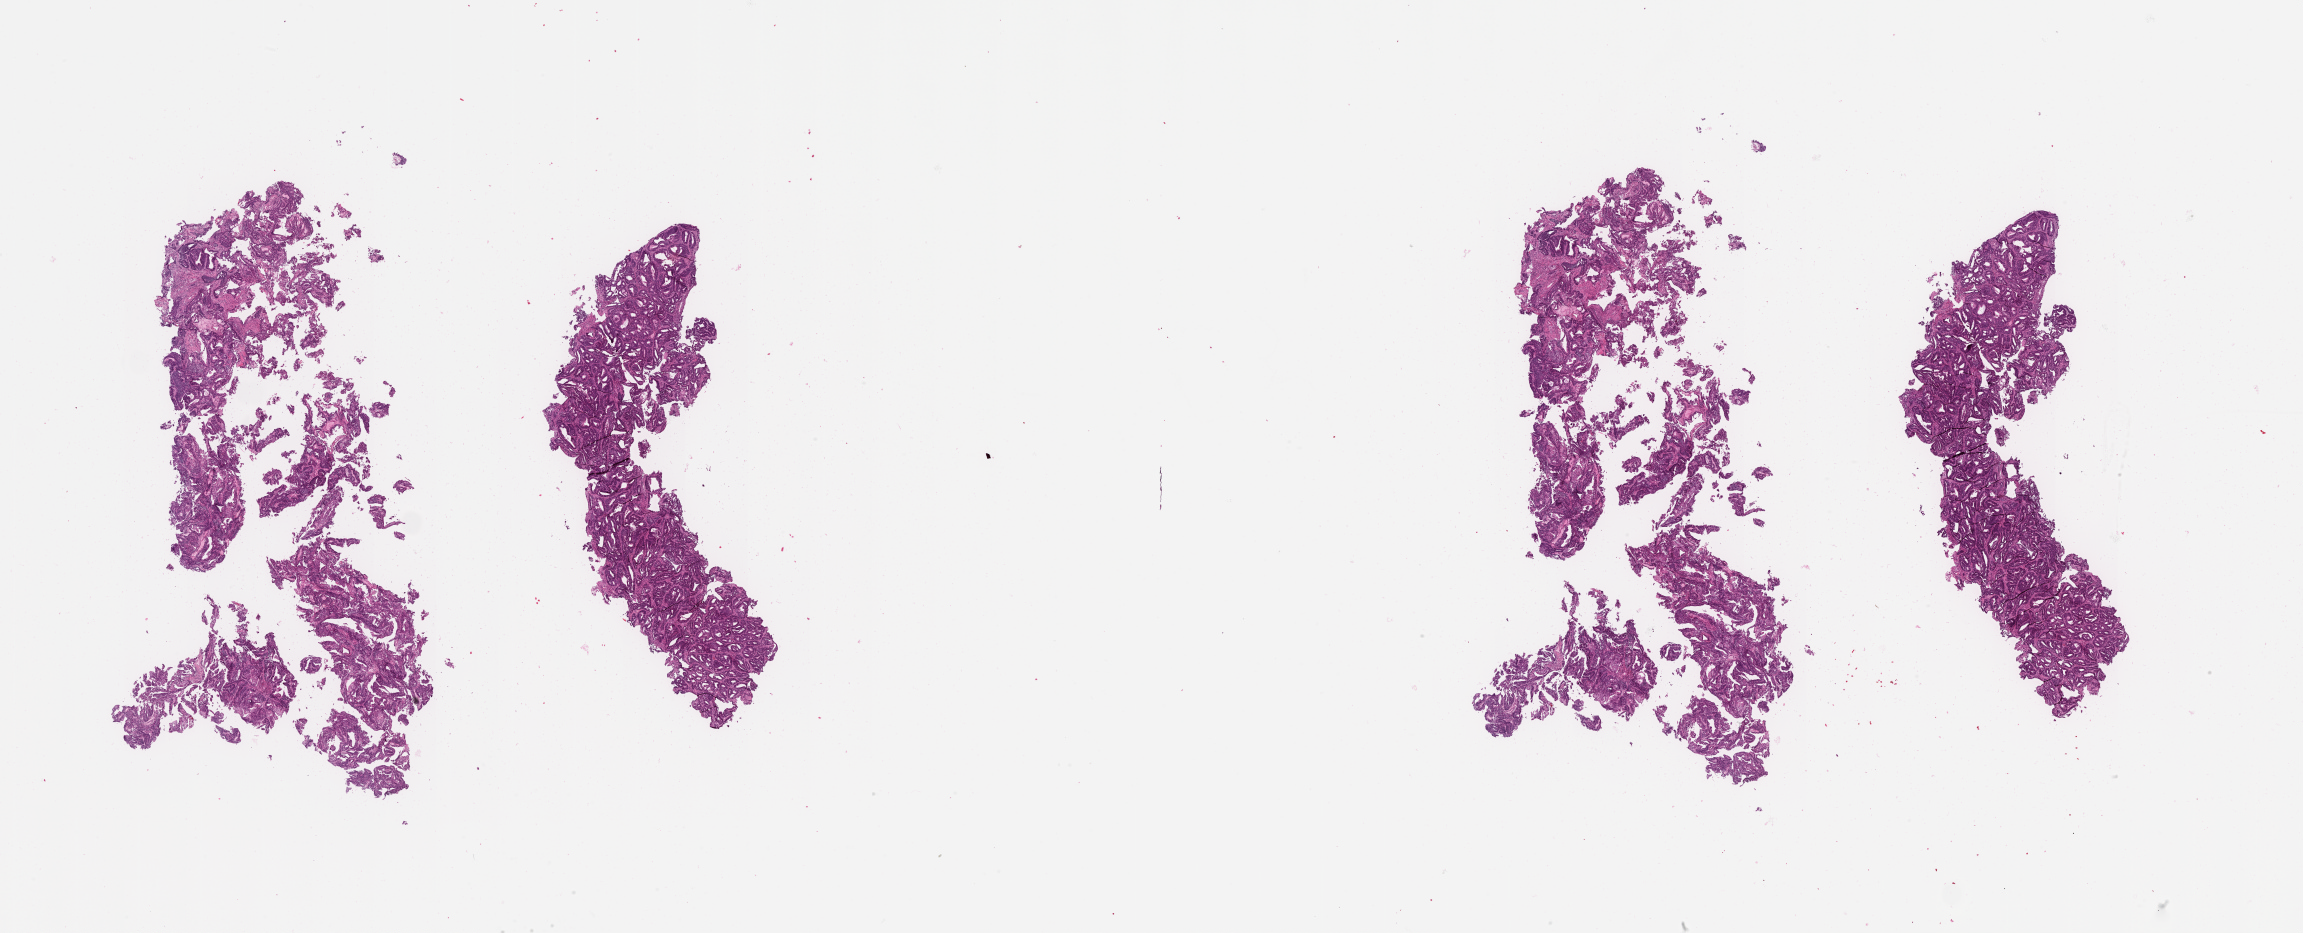
Digitized Hematoxylin and eosin (H&E) stained tissue section (whole slide) — whole scanned area (about 37.1 x 15.0 mm) shown as a low-resolution overview; tumour tissue sample, sampled site: uterus. 44-year-old female patient. Histologic grade: G2 (moderately differentiated). Slide review estimates, as recorded: tumour nuclei 80%, necrosis 0%.
Diagnosis: Endometrioid adenocarcinoma, NOS.